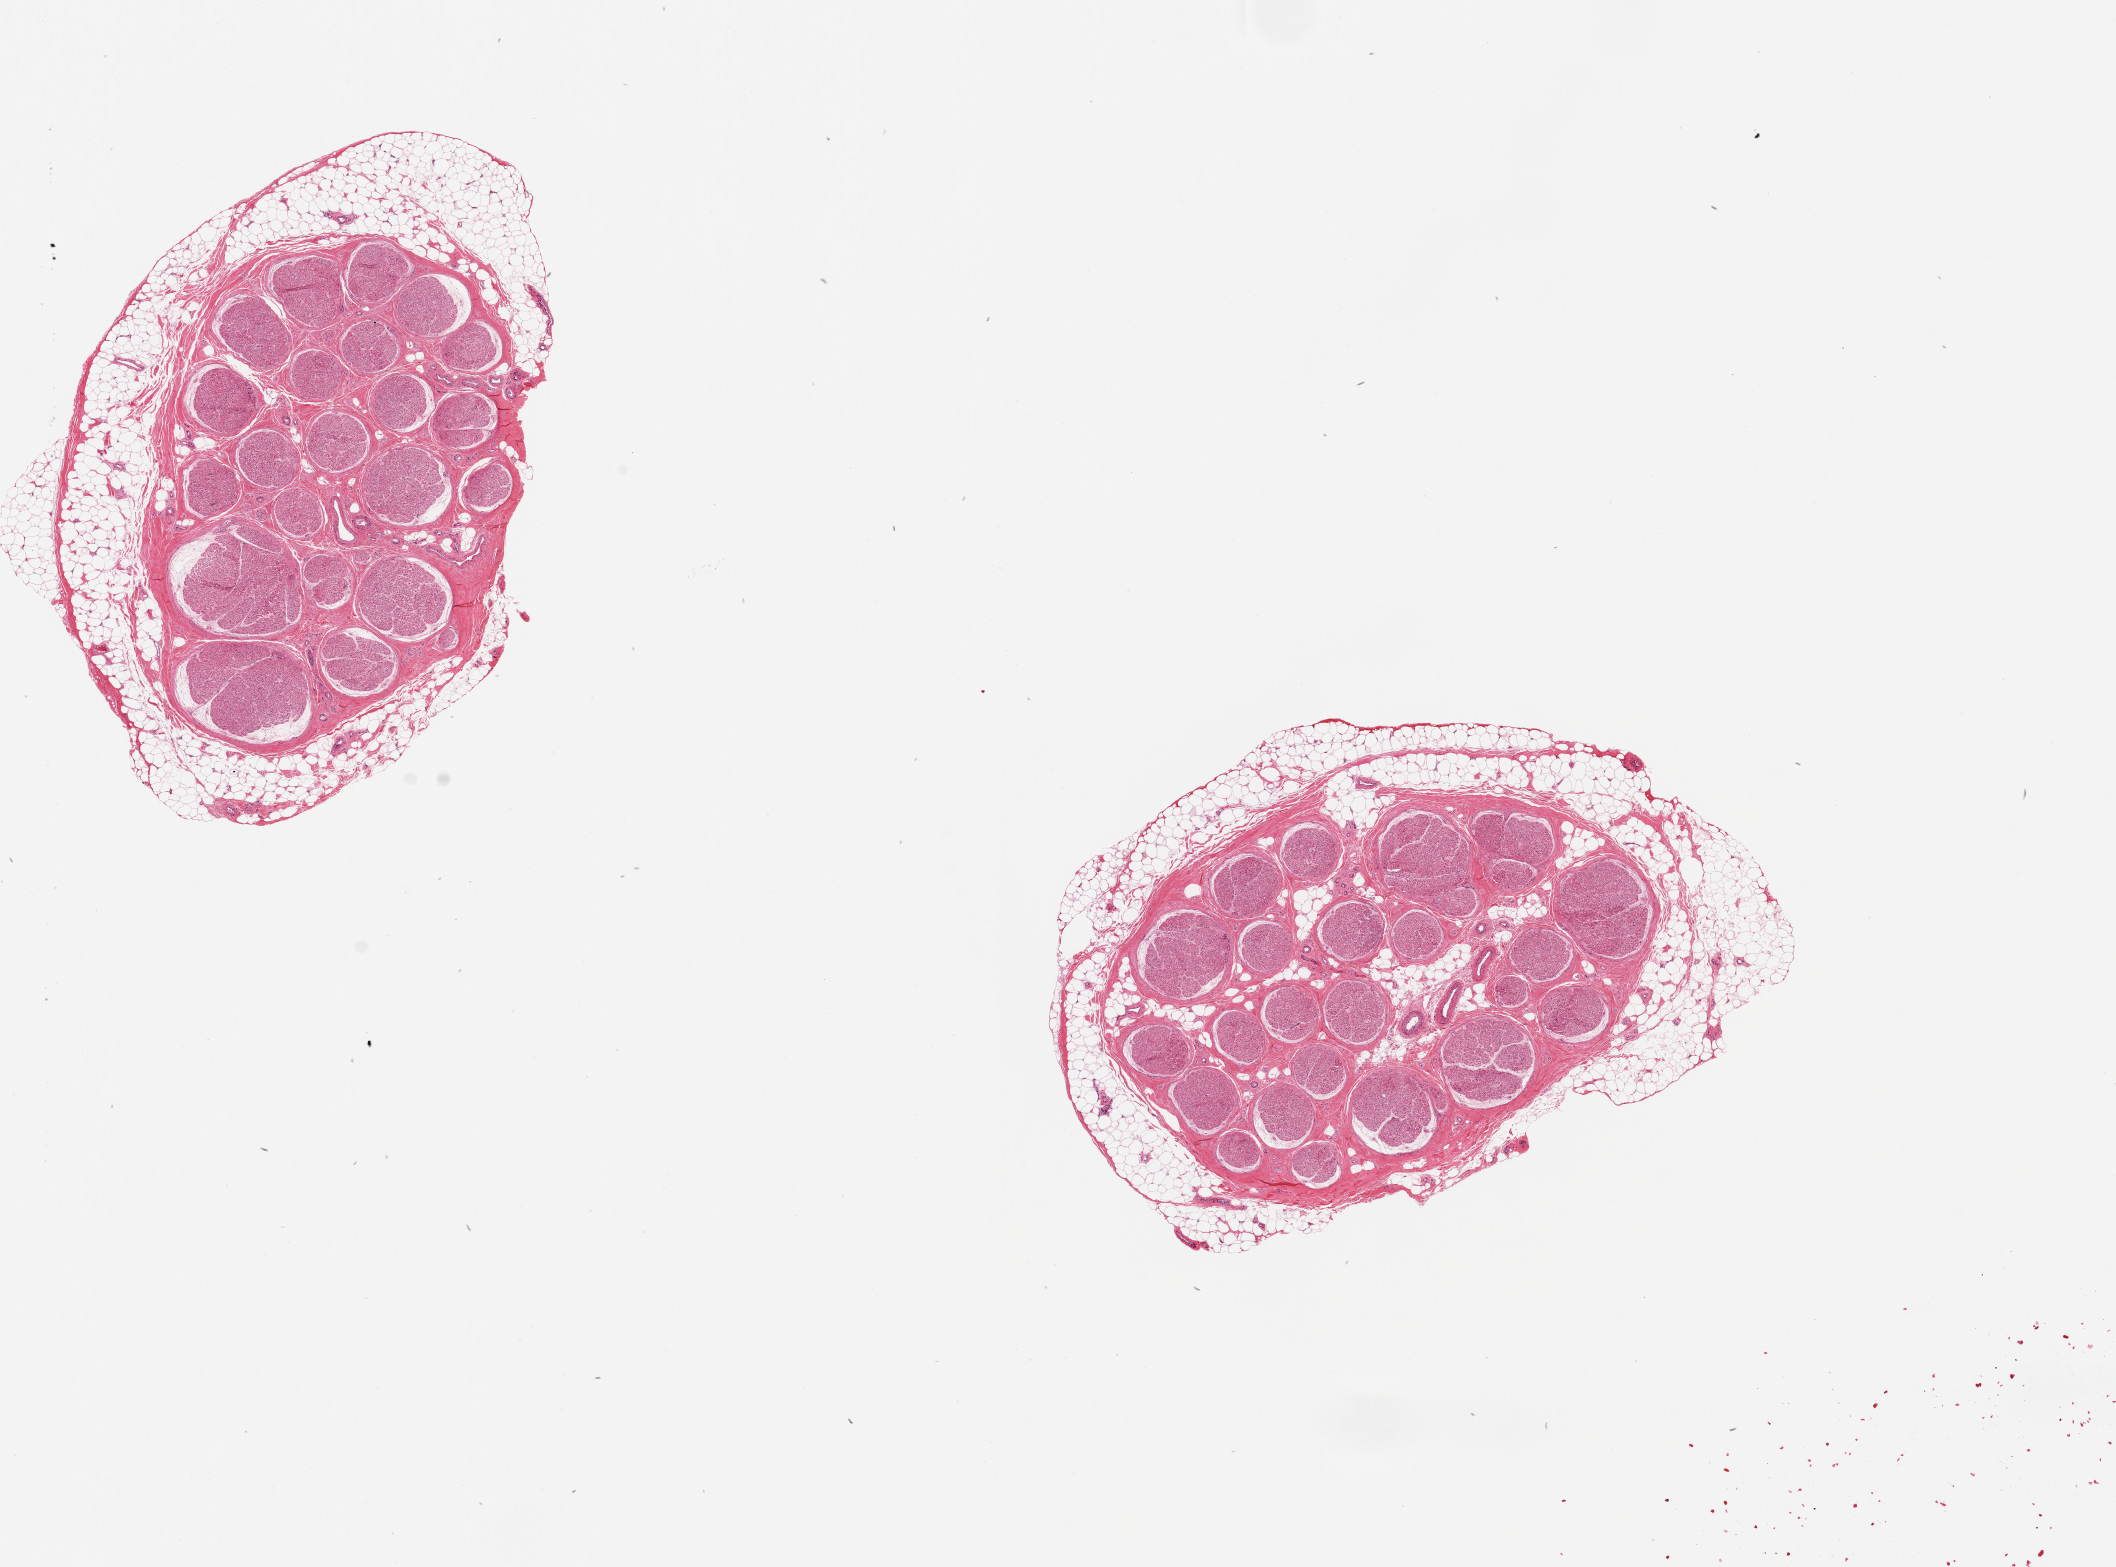
Hematoxylin and eosin (H&E) whole-slide image — low-resolution overview of the scanned area, about 16.7 x 12.4 mm, PAXgene-fixed paraffin-embedded (PFPE) section, sampled site (target tissue): tibial nerve, donor tissue sample. Donor sex: male.
- reviewer comment on this tissue sample: 2 pieces, 6x4 & 6x4mm; 30% peripheral adipose